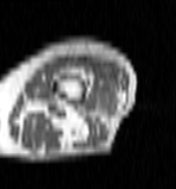
MRI of an extremity soft-tissue mass, one axial slice; position 24 of 100 along the scan axis; MR volume resampled by the dataset authors to the PET/CT grid (not the native acquisition matrix); 3.27 mm slice thickness; 176 × 189 image matrix, field of view 172 × 185 mm. Female patient. From the clinical record (not read from this slice): histological type: undifferentiated – high grade; grade: high; site of the primary tumour: left thigh.
Annotated regions visible in this slice (expert contour drawn on MRI and transferred to this co-registered scan by the dataset authors):
- gross tumour volume including surrounding oedema: bounding box [x1, y1, x2, y2] px = [78, 61, 115, 104]